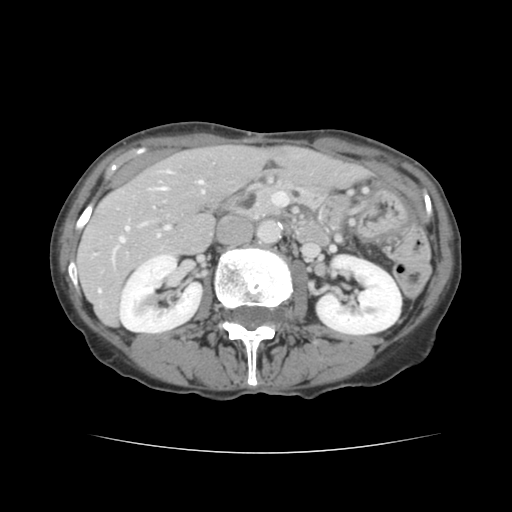
Contrast-enhanced abdominal CT, one axial slice; slice 63 of 136 in the series (ordered by position); 120 kVp; intravenous contrast given; soft-tissue window (W 400 / L 40 HU); 2.5 mm slice thickness; 512 × 512 image matrix, field of view 319 × 319 mm. Female patient, age 77 years. From the clinical record (not read from this slice): diagnosis: colorectal cancer liver metastases, imaged before liver resection; multiple liver metastases: yes; largest metastasis: 3 cm.
Structures marked on this image (expert manual segmentation):
- hepatic veins: bounding box (x1, y1, x2, y2) in pixels: (114, 172, 203, 251)
- liver: (78, 146, 366, 324)
- planned liver remnant (the part of the liver to remain after resection): (162, 146, 365, 206)
- portal vein (with intrahepatic branches): (98, 226, 170, 292)